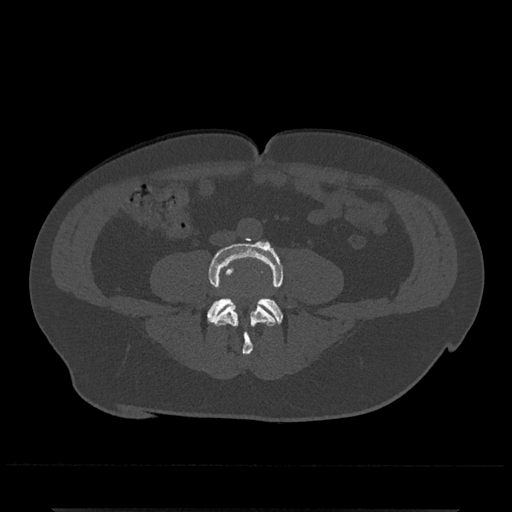
CT including the spine, one axial slice; position 127 of 797 along the scan axis; bone window (W 1800 / L 400 HU); 512 × 512 image matrix, field of view 393 × 393 mm. Male patient, age 67 years. Case-level facts recorded for this patient, not image findings: primary cancer: prostate.
Annotated regions visible in this slice (semi-automatically segmented with operator editing):
- L4 vertebra: bounding box (x1, y1, x2, y2) in pixels: (209, 239, 283, 355)
- L5 vertebra: (208, 297, 283, 323)